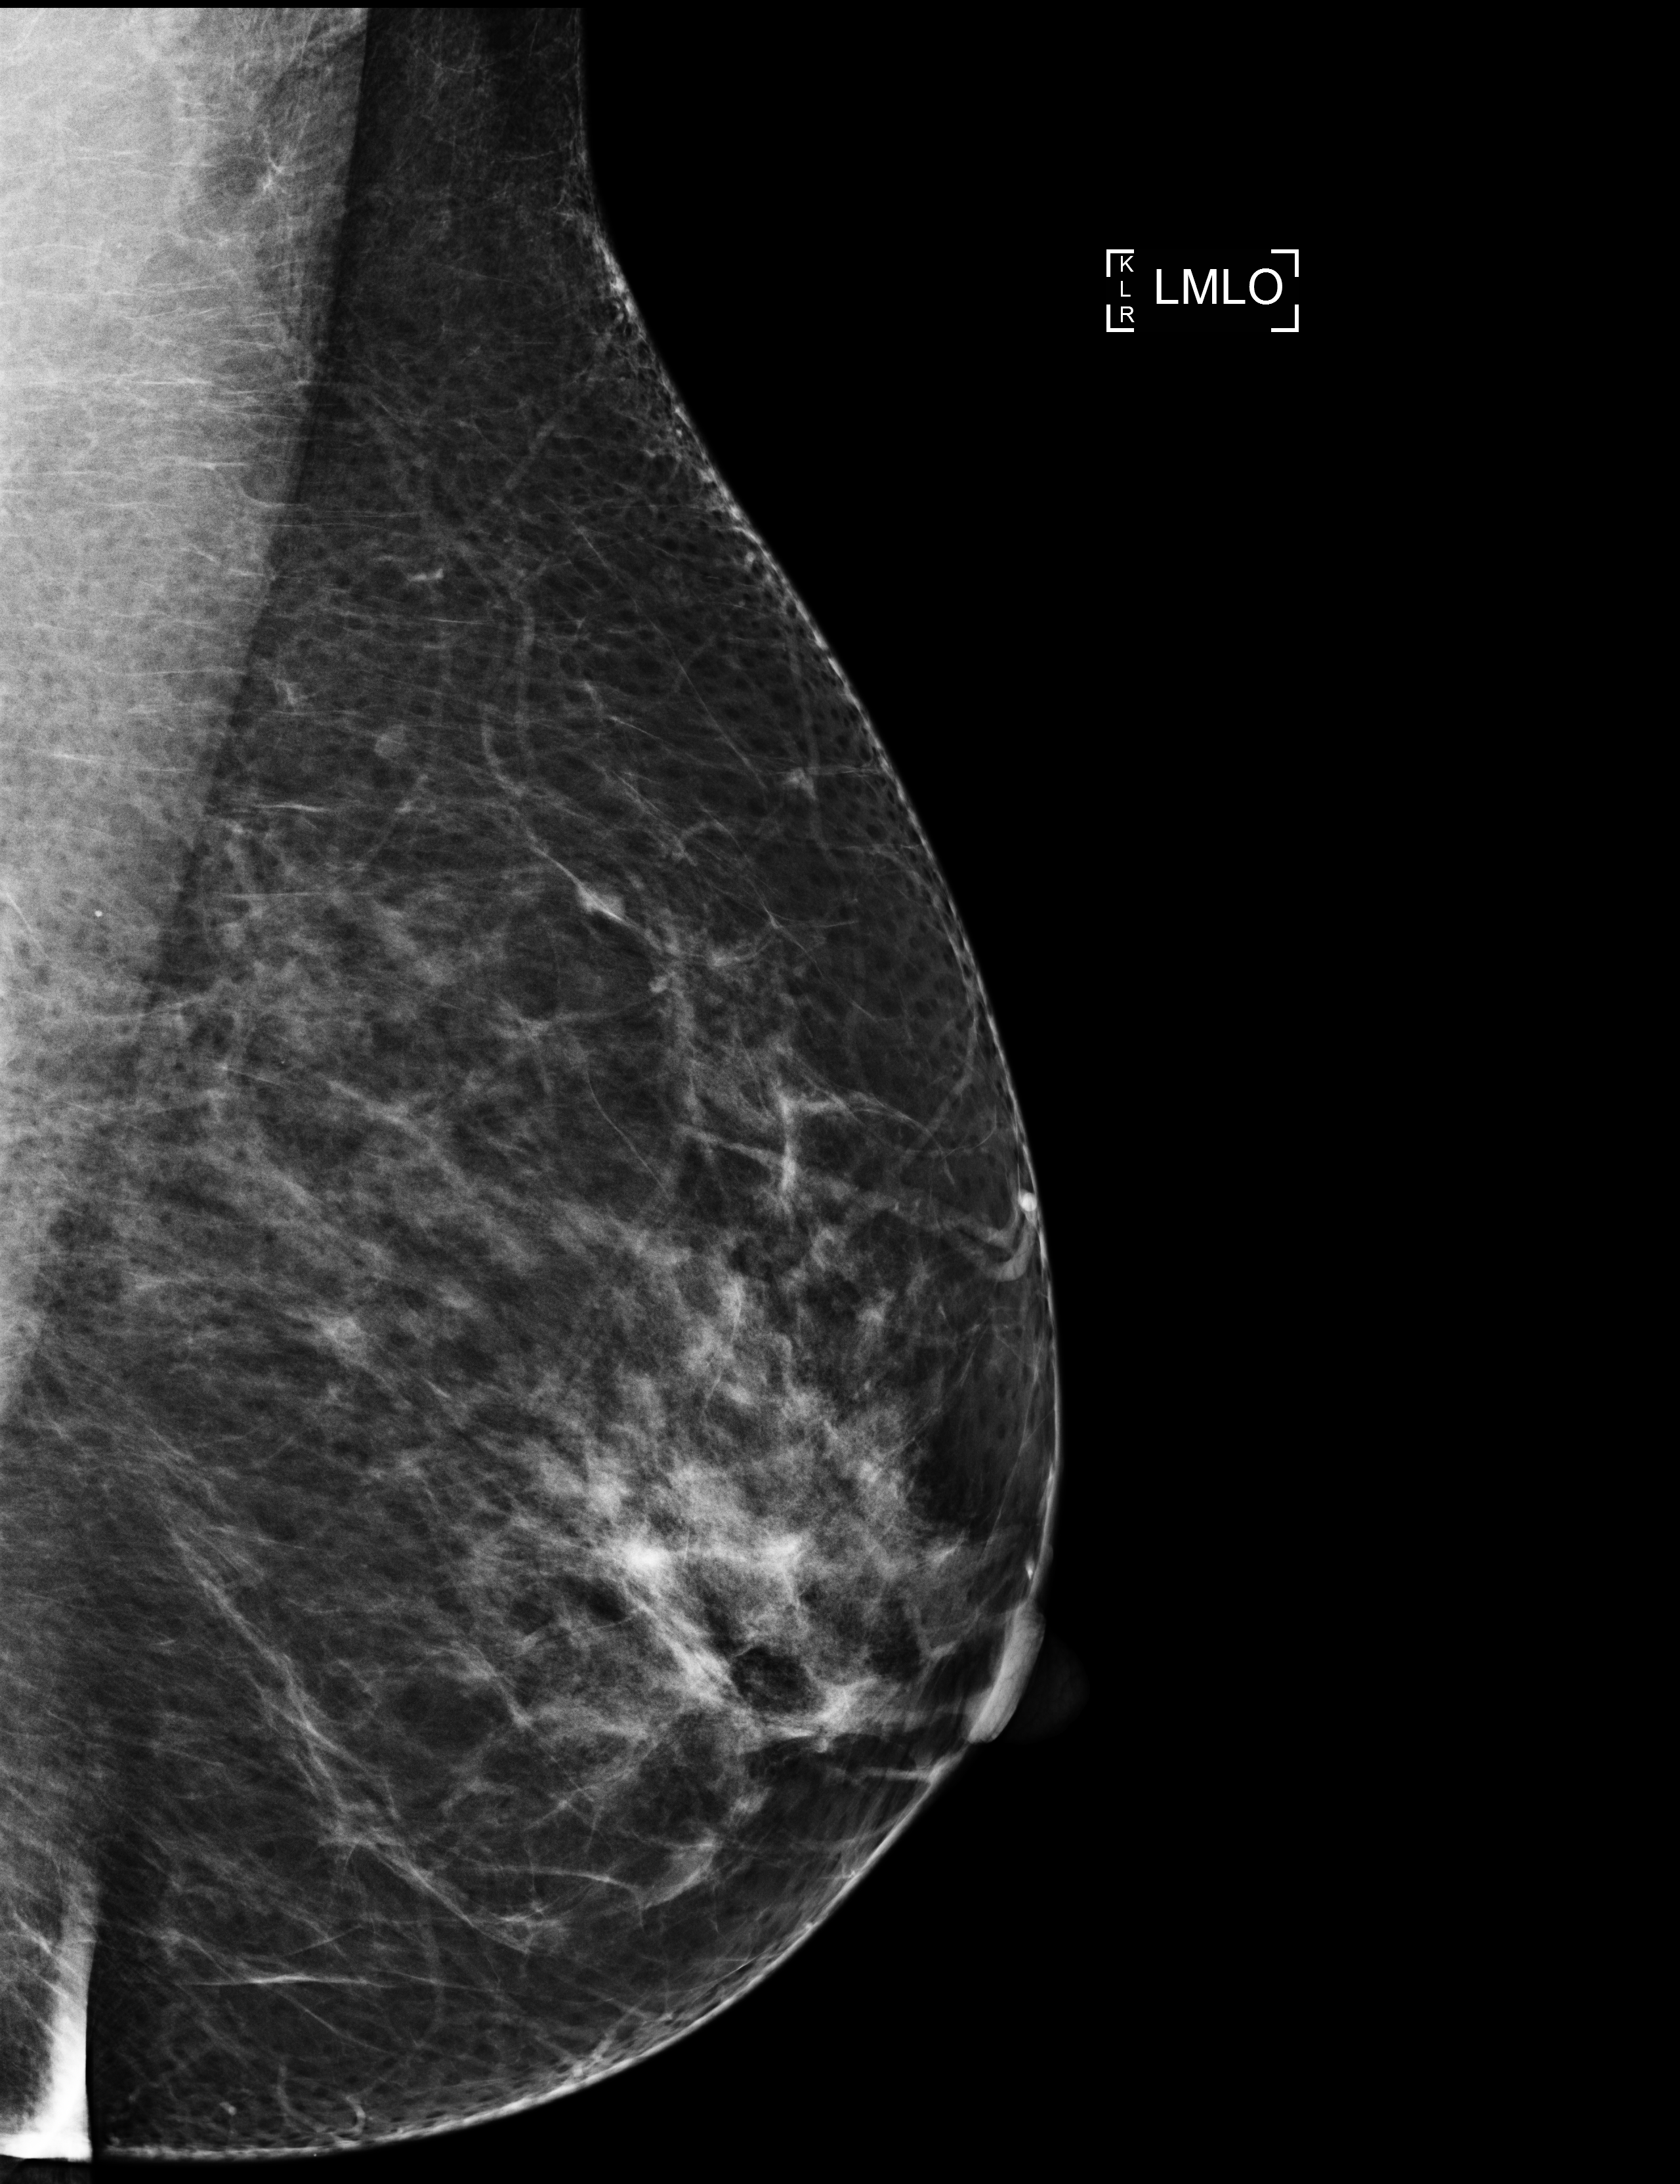
Annual screening mammography examination; compressed breast thickness 87 mm. Patient: female, 51 years.
Image type: full-field digital mammogram. Breast: left. Projection: mediolateral oblique (MLO) view.